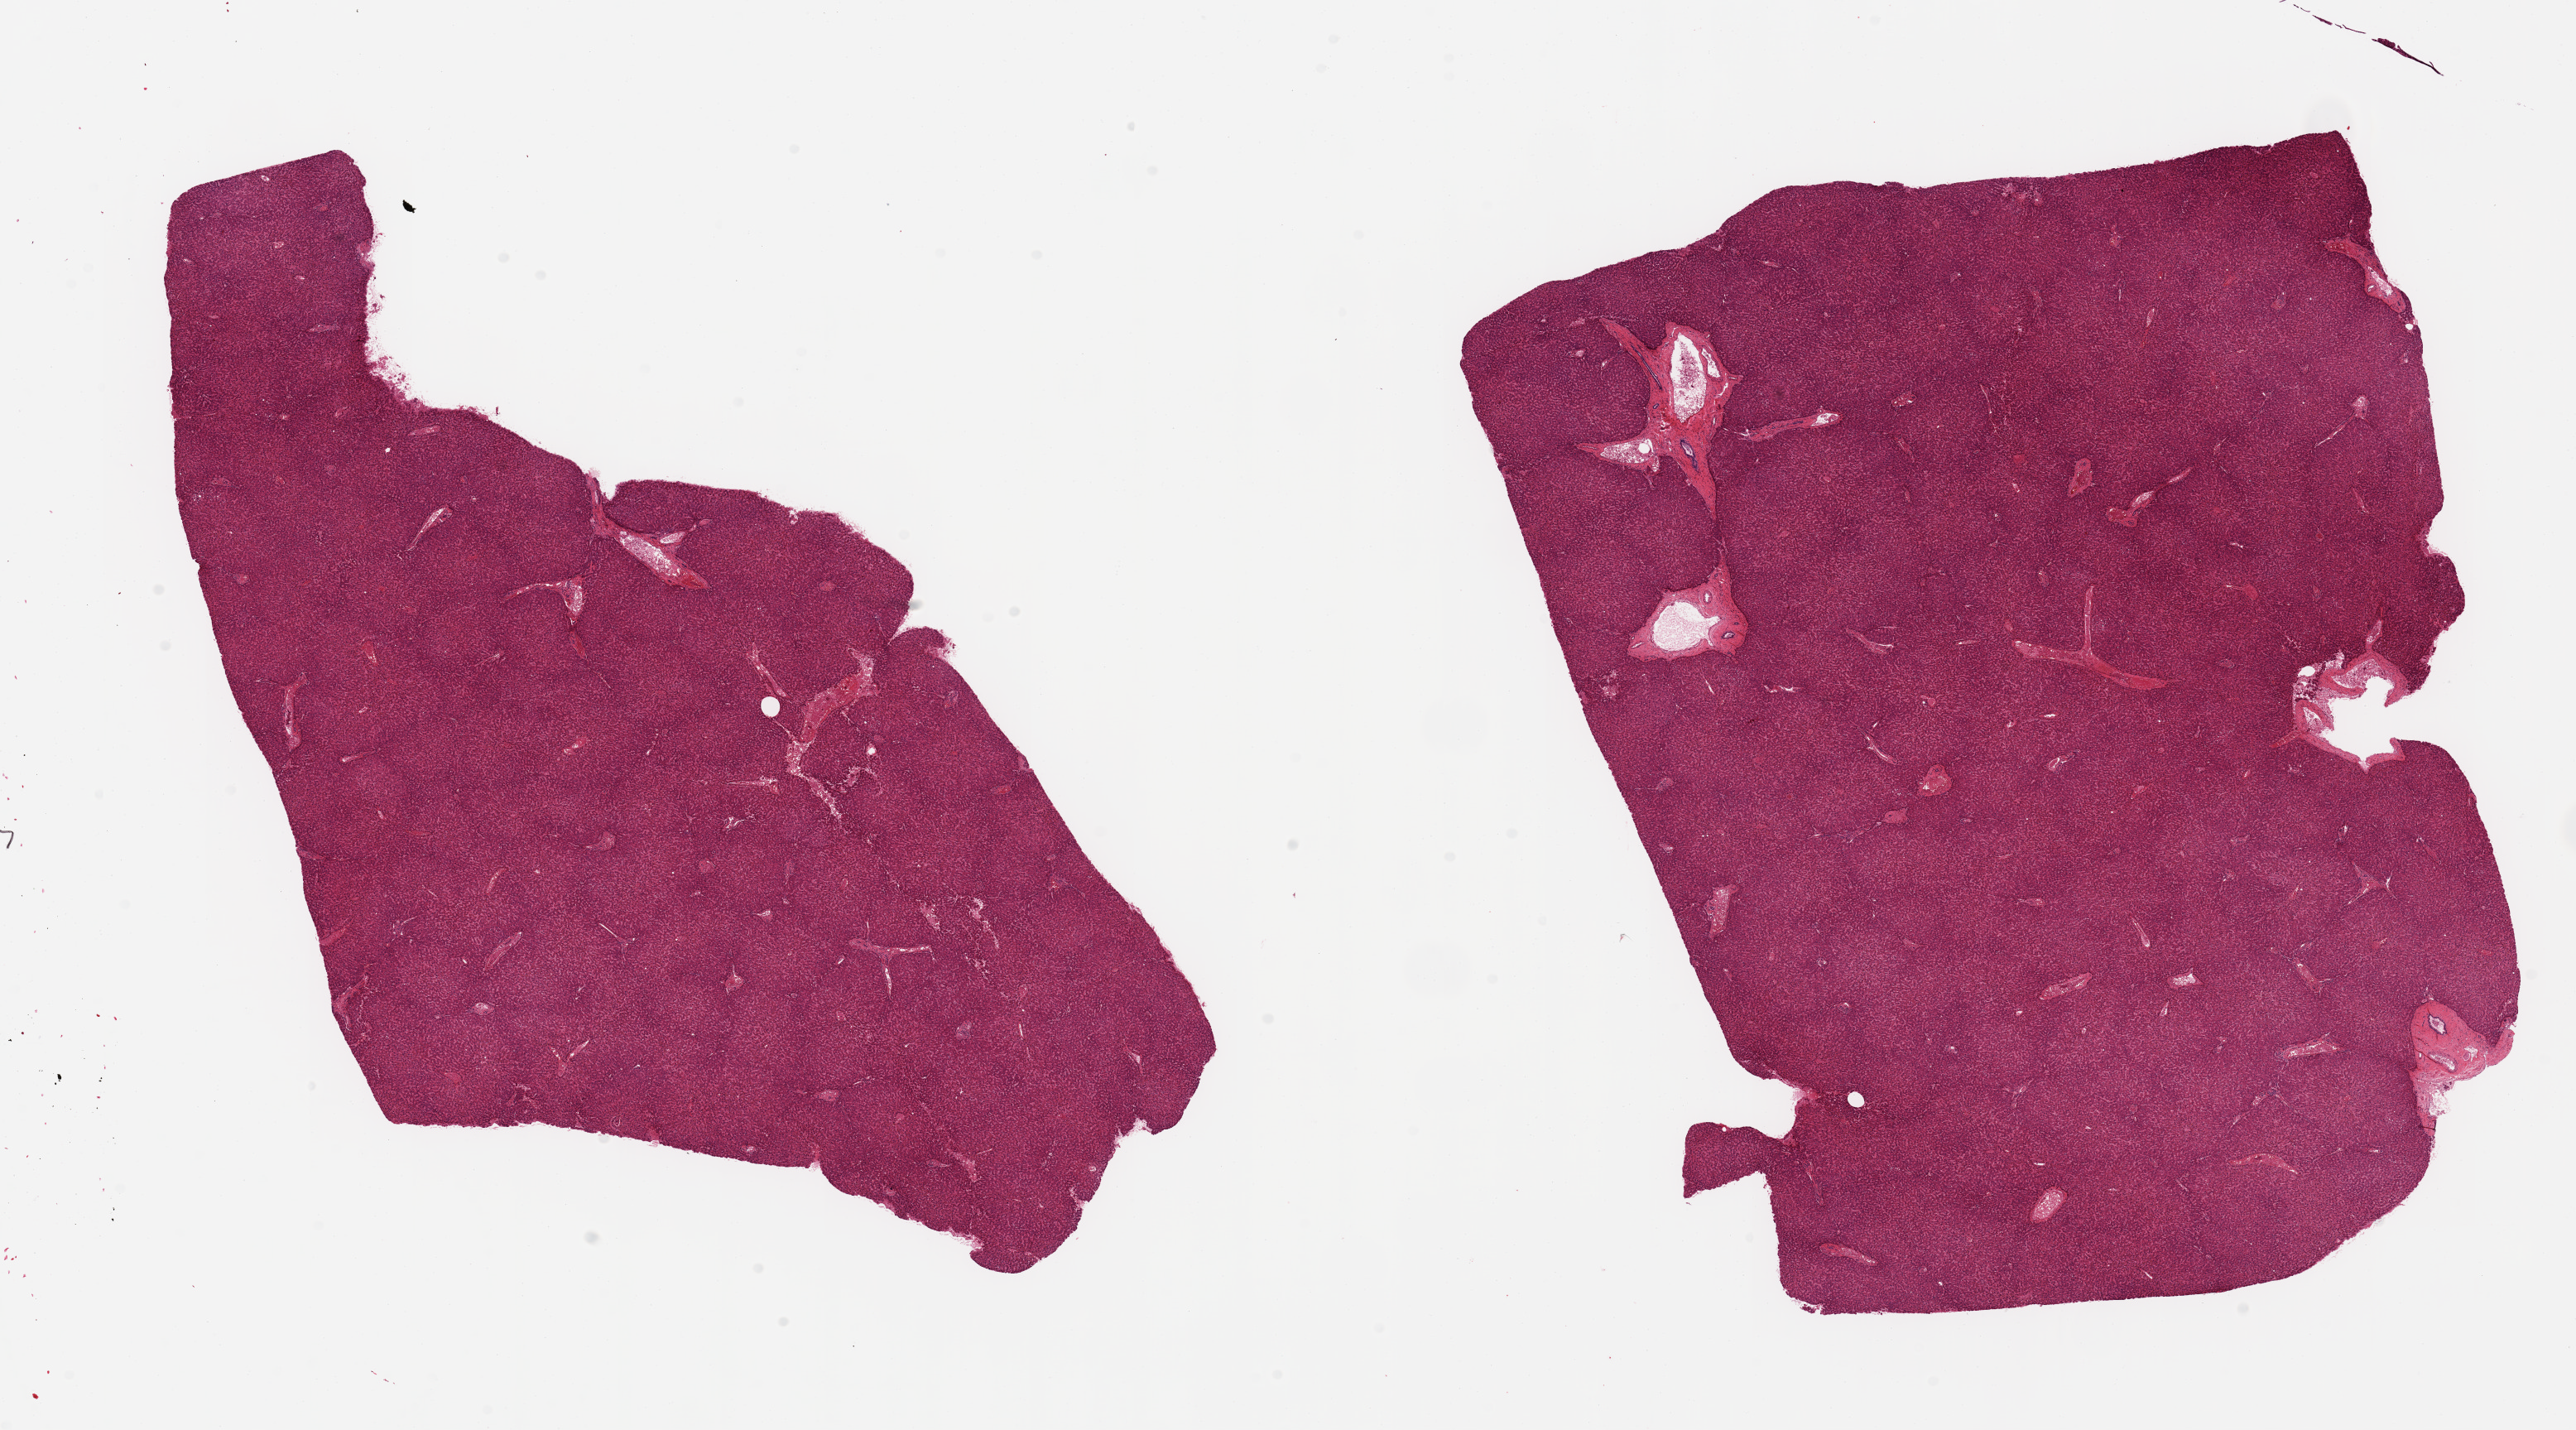
Hematoxylin and eosin (H&E) whole-slide image, low-resolution overview of the scanned area, about 24.6 x 13.7 mm, PAXgene-fixed, paraffin-embedded tissue, target tissue: liver, donor tissue sample. Donor sex: male.
Review note (as recorded): 2 pieces, mild microvesicular steatosis.